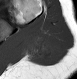
MRI of an extremity soft-tissue mass, one axial slice; position 16 of 28 along the scan axis; MR volume resampled by the dataset authors to the PET/CT grid (not the native acquisition matrix); 77 × 79 image matrix, field of view 75 × 77 mm. Female patient. From the clinical record (not read from this slice): histological type: malignant fibrous histiocytoma; grade: low; site of the primary tumour: left arm.
Outlined on this slice (expert contour drawn on MRI and transferred to this co-registered scan by the dataset authors):
- gross tumour volume (mass): bounding box <26,32,54,60> (left, top, right, bottom; pixels)